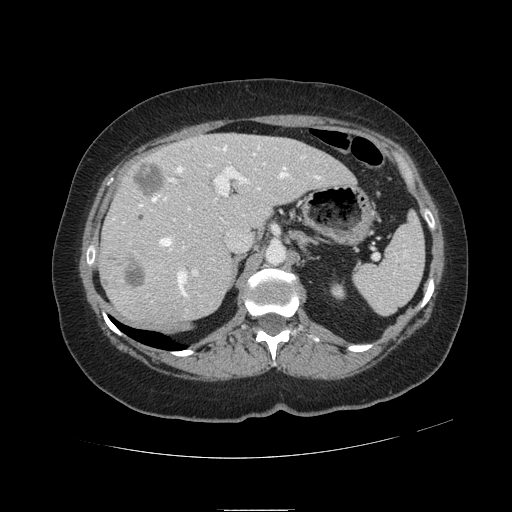
Contrast-enhanced abdominal CT, one axial slice; slice 70 of 121 in the series (ordered by position); 120 kVp; intravenous contrast given; soft-tissue window (W 400 / L 40 HU); 2.5 mm slice thickness; 512 × 512 image matrix, field of view 400 × 400 mm. Female patient, age 52 years. Case-level facts recorded for this patient, not image findings: diagnosis: colorectal cancer liver metastases, imaged before liver resection; multiple liver metastases: yes; largest metastasis: 6.3 cm; disease in both lobes: no.
Annotated regions visible in this slice (expert manual segmentation):
- hepatic veins: bounding box [x1, y1, x2, y2] px = [113, 146, 322, 297]
- liver: [100, 134, 353, 322]
- planned liver remnant (the part of the liver to remain after resection): [167, 134, 353, 227]
- portal vein (with intrahepatic branches): [123, 162, 266, 276]
- liver metastasis: [131, 162, 165, 196]
- liver metastasis: [126, 261, 145, 289]